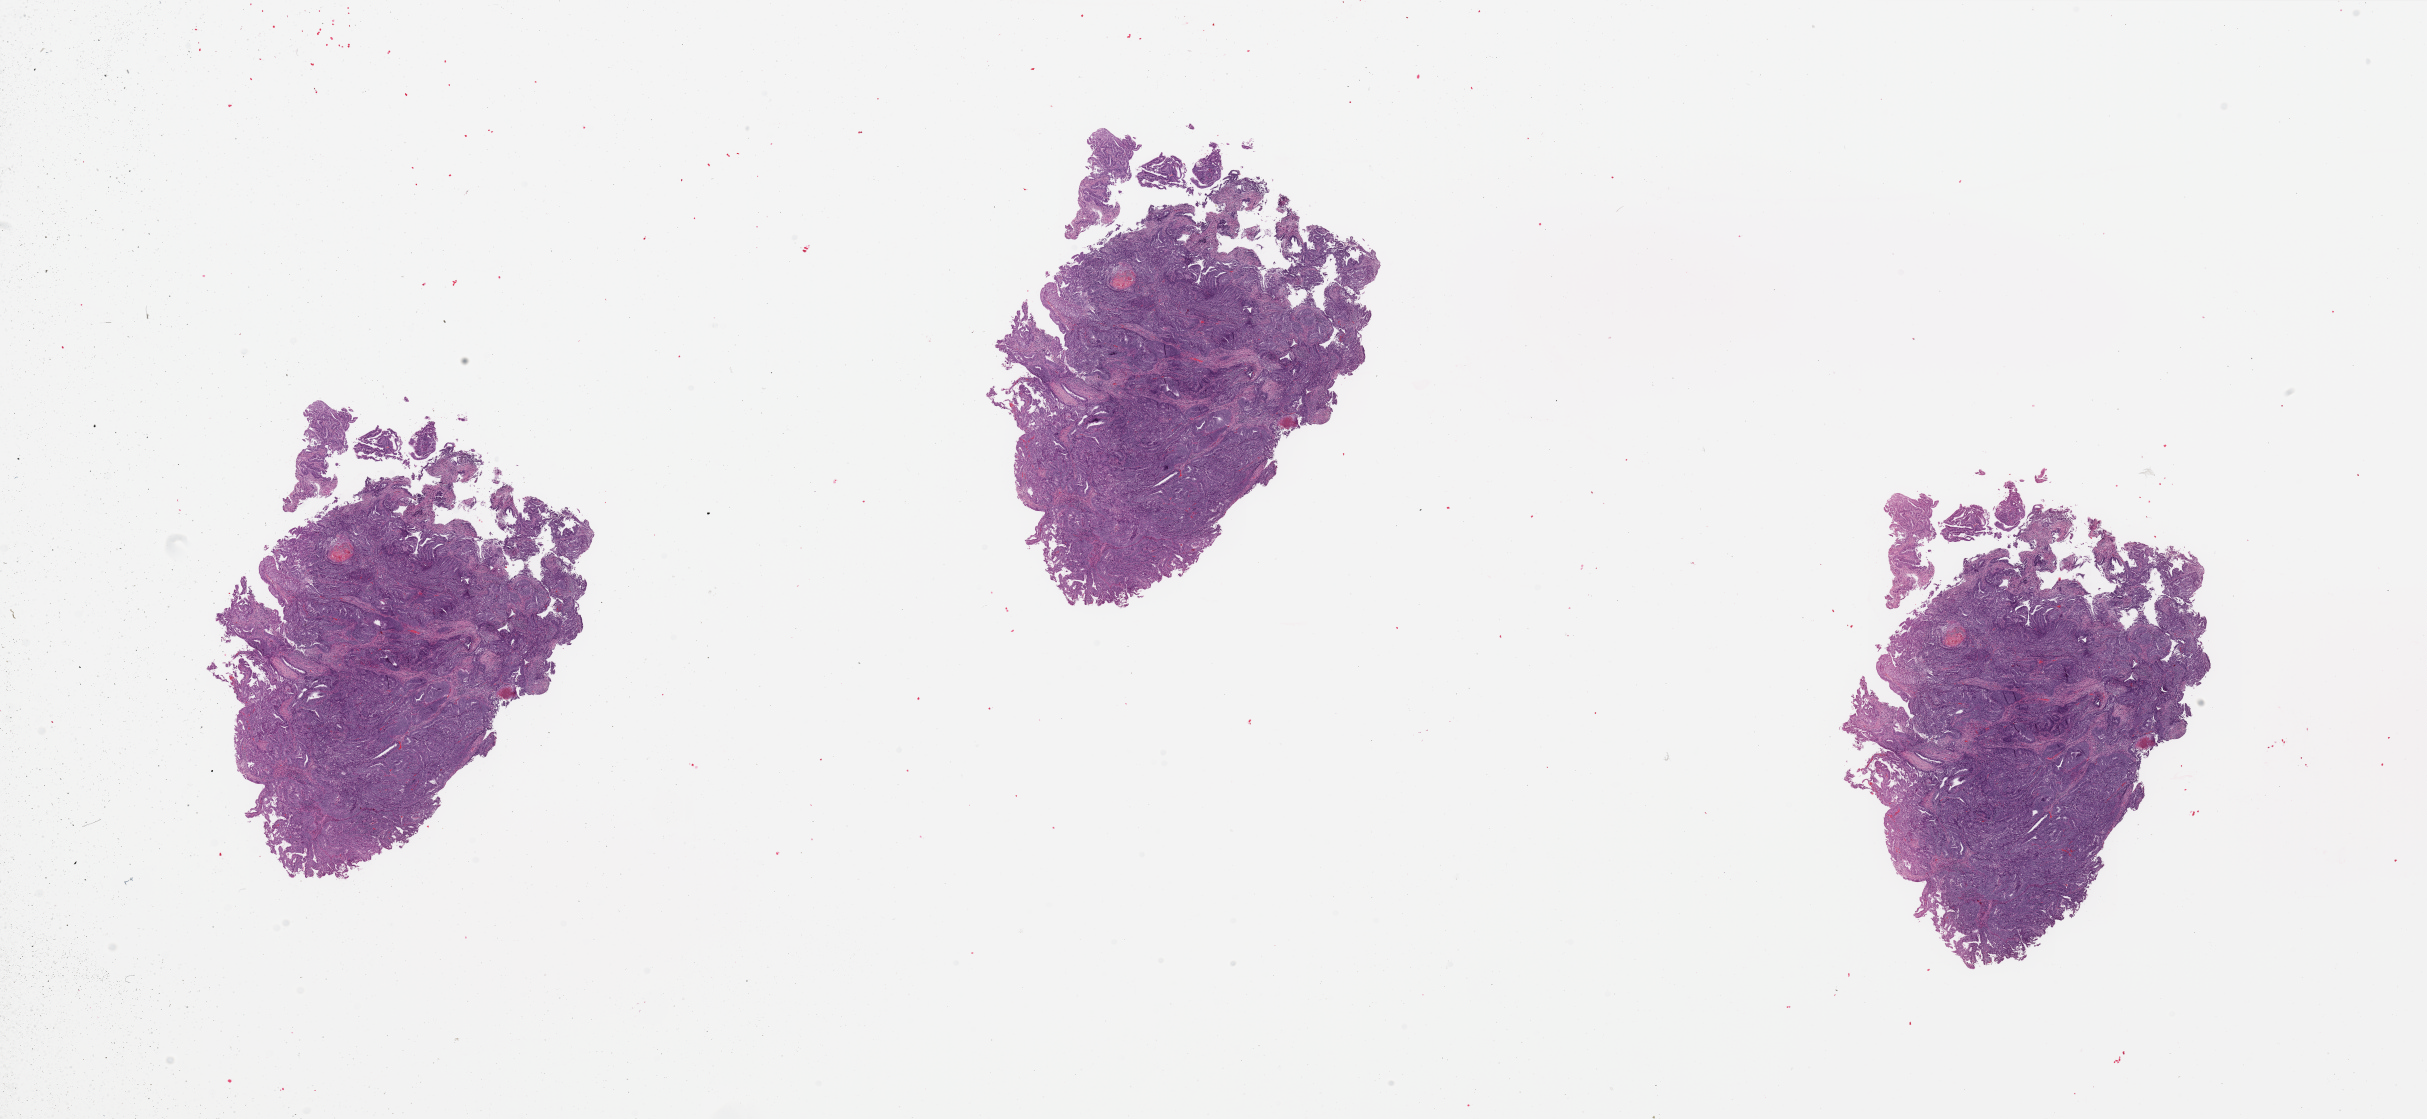
Digitized Hematoxylin and eosin (H&E) stained tissue section (whole slide) — whole scanned area (about 38.4 x 17.7 mm, acquisition: 20x scan) shown as a low-resolution overview, tumour tissue sample, sampled site: uterus. Patient: female, age 39 years. Histologic grade: G2 (moderately differentiated). Pathologist review of this section (percent, as recorded): tumour nuclei 90%, necrosis 2%.
- diagnosis: Endometrioid adenocarcinoma, NOS
- AJCC pathologic stage: I